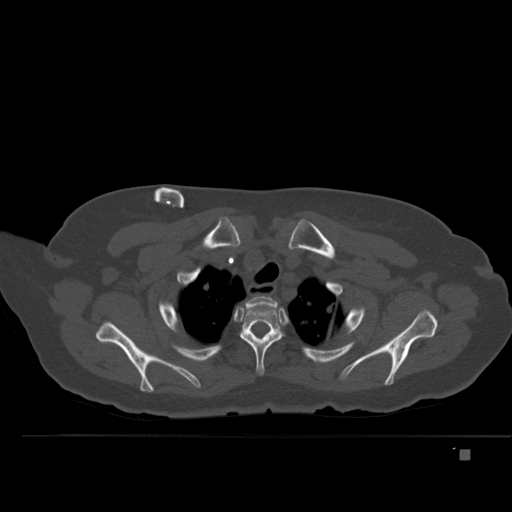
CT including the spine, one axial slice. Position 391 of 477 along the scan axis. Bone window (W 1800 / L 400 HU). 1.5 mm slice thickness. 512 × 512 image matrix, field of view 422 × 422 mm. Patient: female, 74 years. From the clinical record (not read from this slice): primary cancer: colon.
Annotated regions visible in this slice (semi-automatically segmented with operator editing):
- T1 vertebra: bounding box <235,296,277,321> (left, top, right, bottom; pixels)
- T2 vertebra: <240,307,288,376>